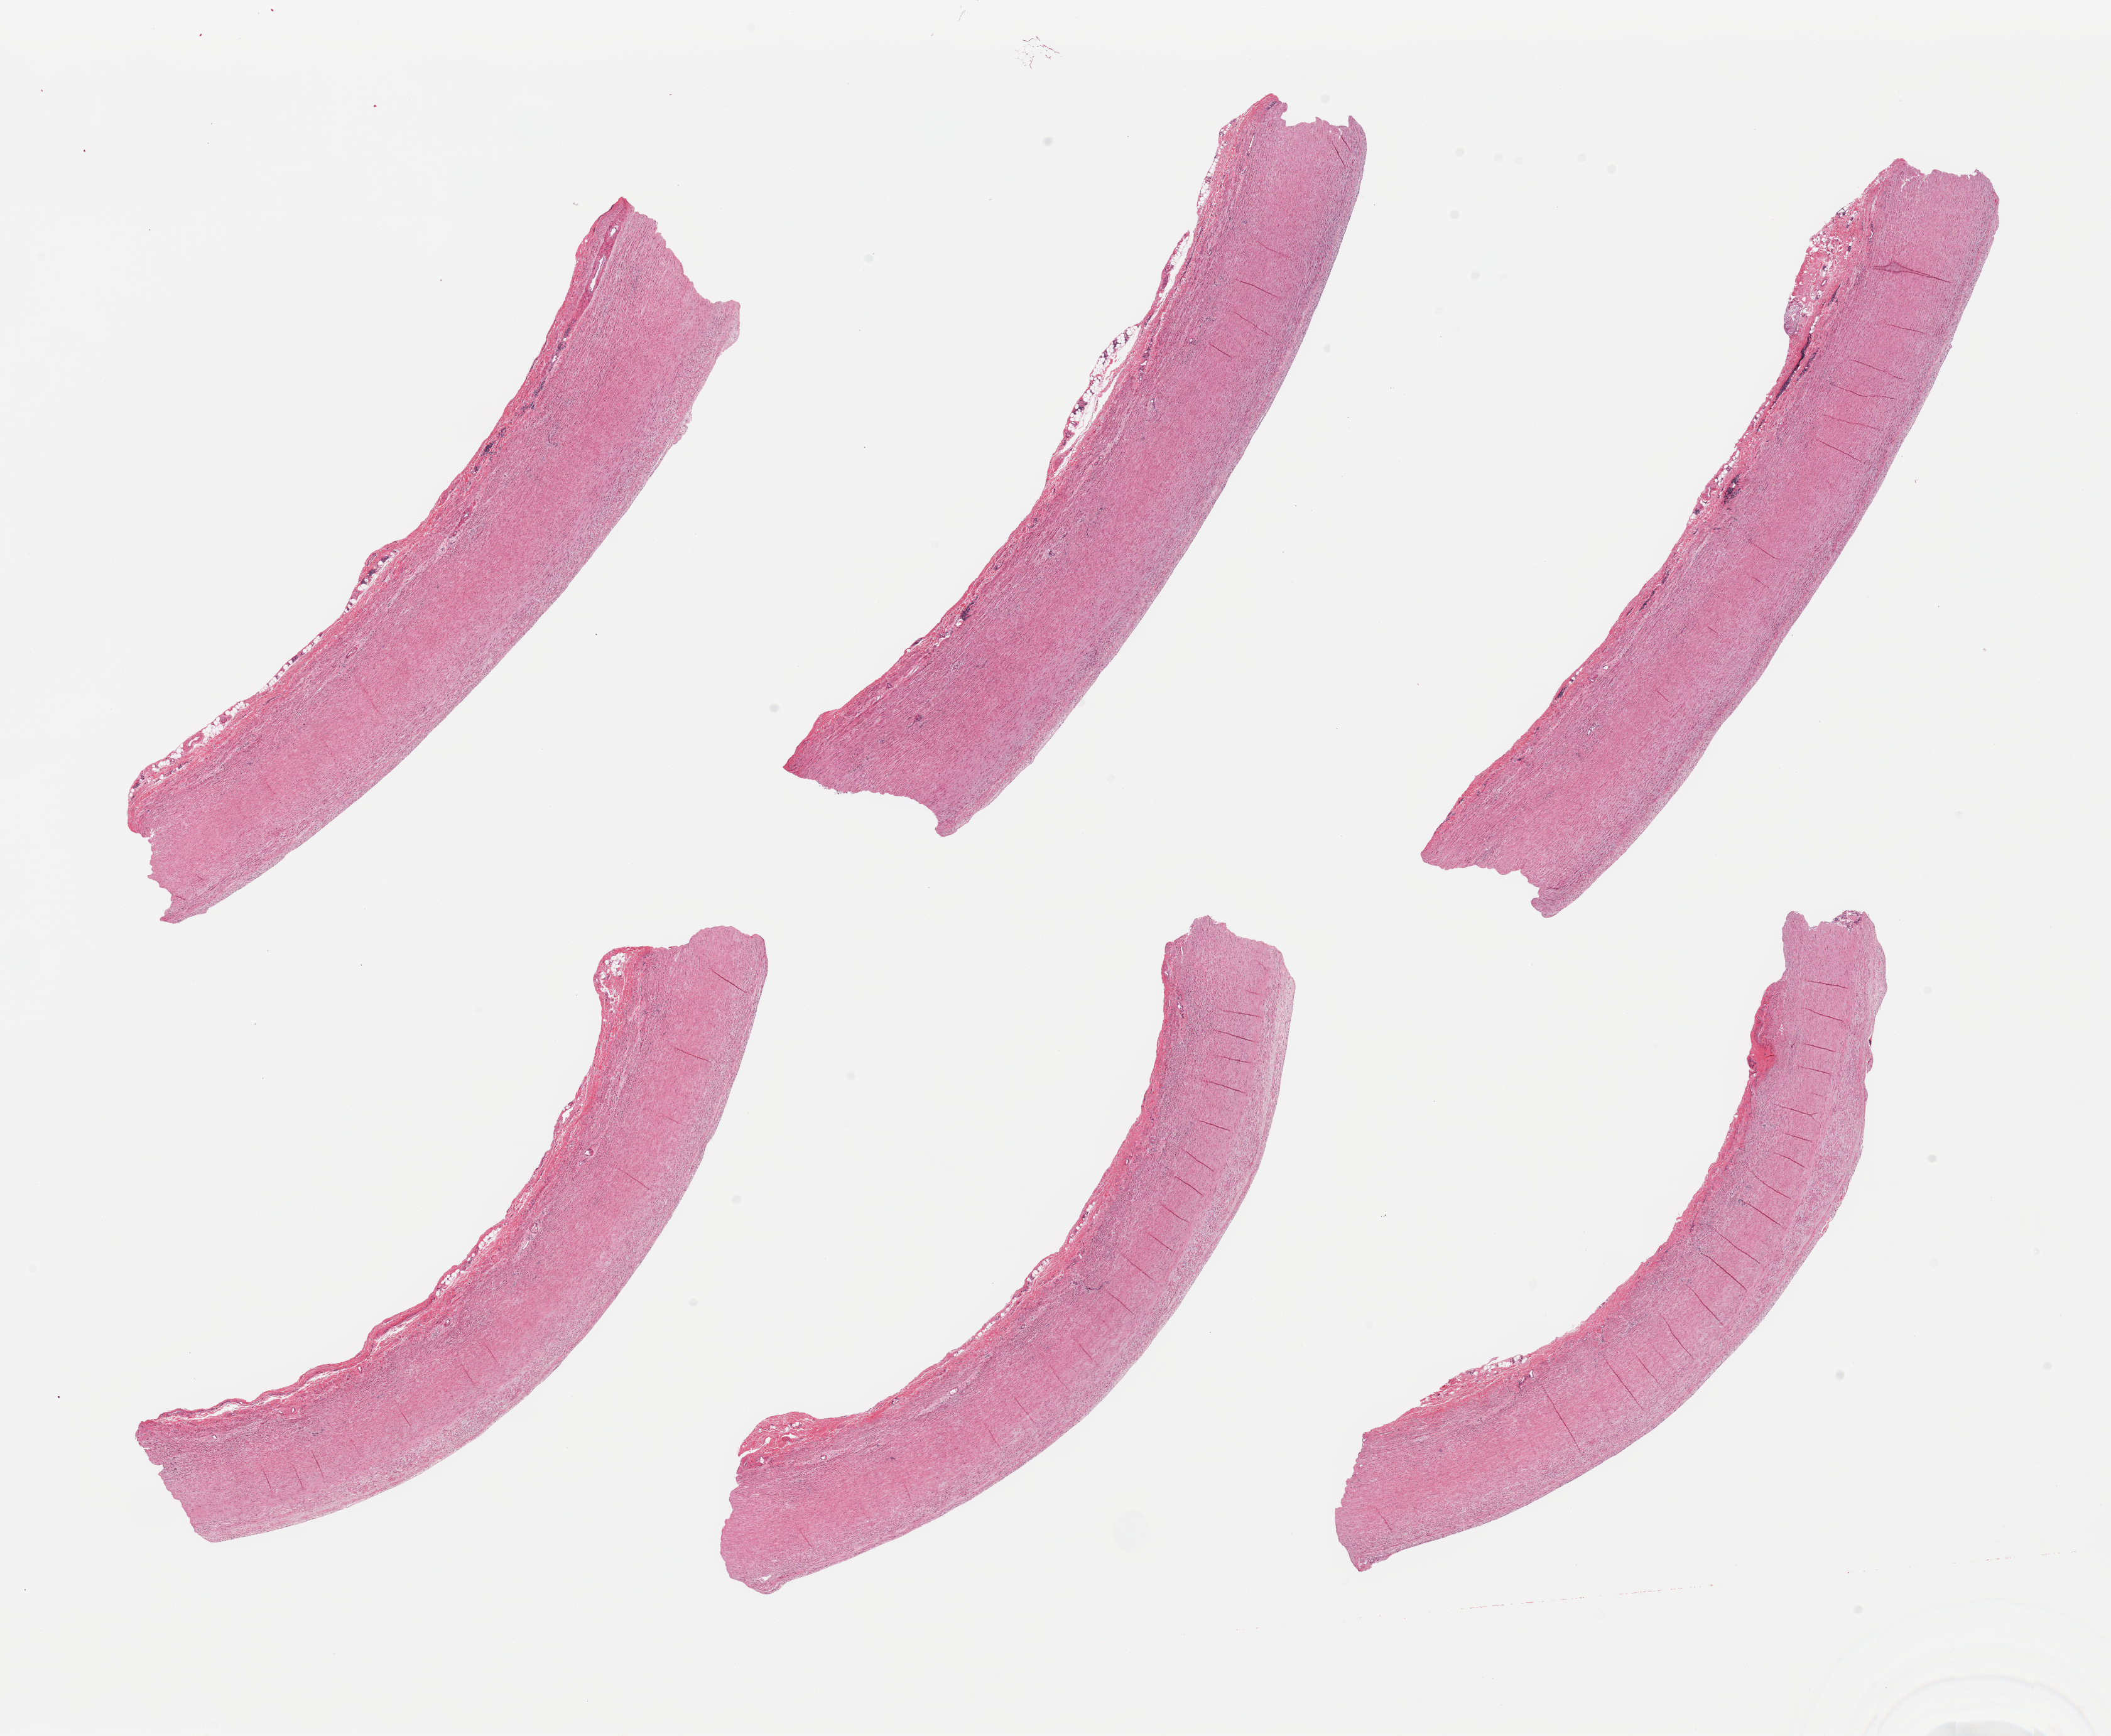
Whole-slide image, haematoxylin and eosin stain, brightfield, low-resolution overview of the scanned area, about 26.6 x 21.9 mm; PAXgene-fixed paraffin-embedded (PFPE) section; target tissue: aorta; tissue donor sample. Donor: female.
Pathologist's review note for this sample: 6 pieces, minimal atherosis.